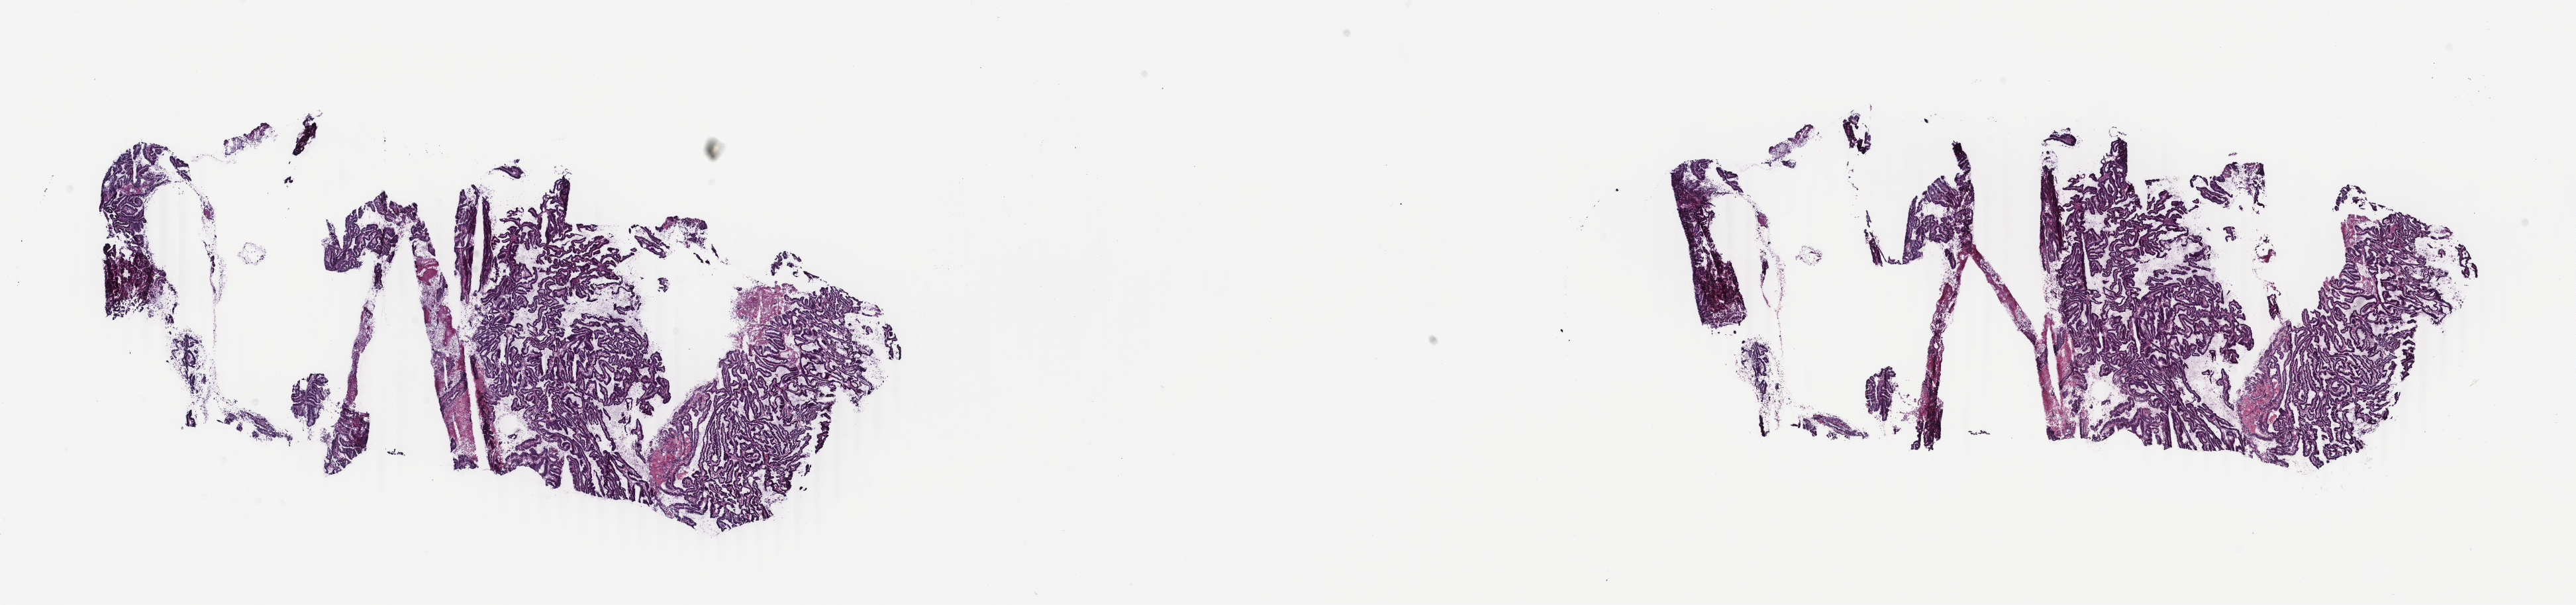
Hematoxylin and eosin (H&E) stained whole-slide image — shown as a low-resolution overview of the whole scanned area (about 30.9 x 7.3 mm). Frozen section from the bottom of the tissue portion. Sample: primary tumour, uterus. Female, age 64 years at initial diagnosis.
Diagnosis: Endometrioid adenocarcinoma, NOS (endometrium).